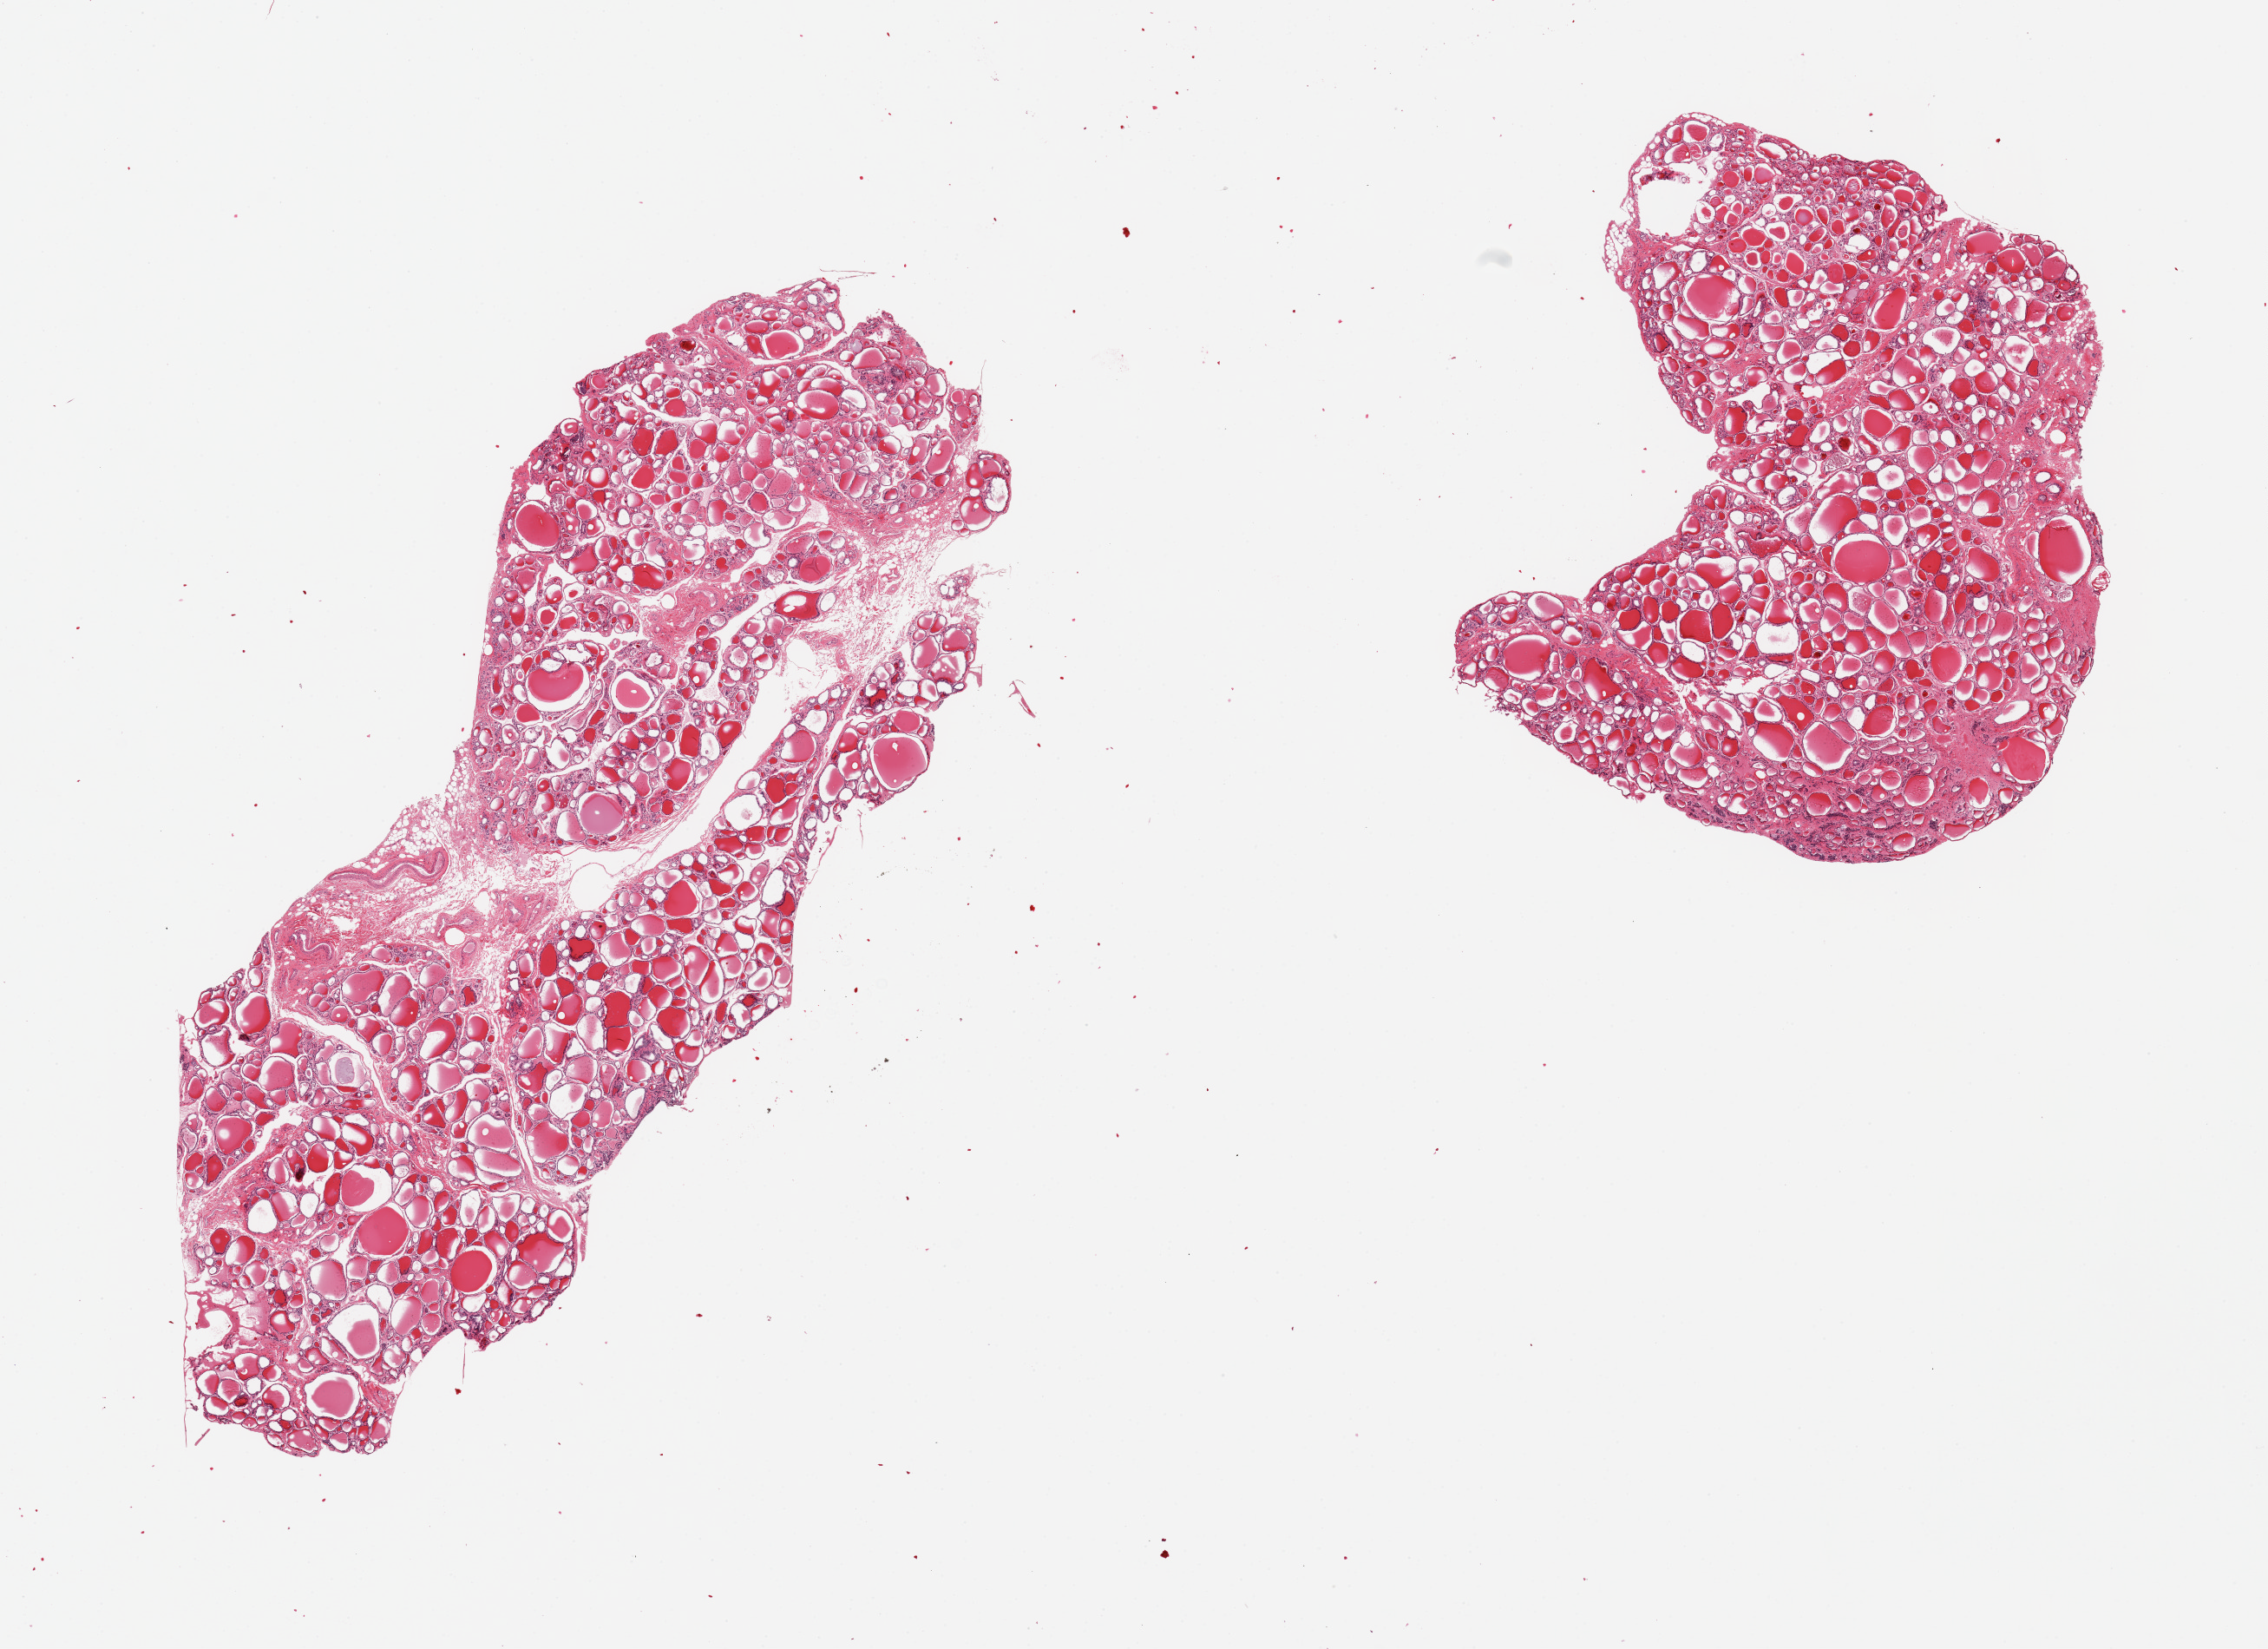
Digitized haematoxylin and eosin-stained section, brightfield — whole scanned area (about 20.7 x 15.0 mm, slide scanned at 20x) shown as a low-resolution overview; PAXgene-fixed paraffin-embedded (PFPE) section; sampled site (target tissue): thyroid; donor tissue sample. Donor: male.
Reviewer comment on this tissue sample: 2 pieces, no significant abnormalities.